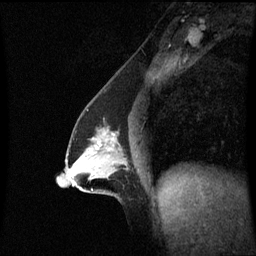
Breast MRI (dynamic contrast-enhanced), one sagittal slice. Slice 33 of 60 in the series (ordered by position). Dynamic contrast-enhanced series, image 2 of 3 at this slice position (ordered by acquisition). 1.5 T. TE 4.2 ms, TR 8.9 ms. 256 × 256 image matrix, field of view 210 × 210 mm. Patient: female, 47 years. Case-level facts recorded for this patient, not image findings: setting: breast cancer imaged before/during neoadjuvant chemotherapy; receptor status: HR-positive, HER2-negative.
Annotated regions visible in this slice (semi-automatic segmentation, software-assisted and operator-edited):
- analysis volume of interest (the breast-tissue region the enhancement analysis was run in; not a lesion): box from (x=64, y=125) to (x=129, y=196) px
- tumour enhancement mask (voxels above the 70 % enhancement threshold inside the analysis volume of interest): (x=96, y=138)–(x=116, y=152)